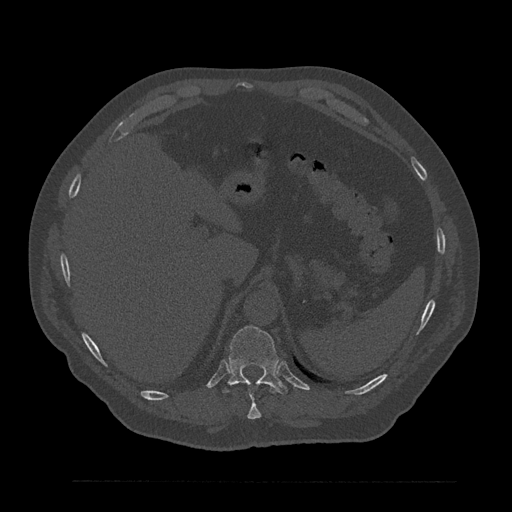
CT including the spine, one axial slice. Position 312 of 797 along the scan axis. 120 kVp. Bone window (W 1800 / L 400 HU). 512 × 512 image matrix, field of view 430 × 430 mm. Patient: male, 61 years. From the clinical record (not read from this slice): primary cancer: prostate.
Outlined on this slice (semi-automatically segmented with operator editing):
- T10 vertebra: box from (x=247, y=392) to (x=262, y=420) px
- T11 vertebra: (x=223, y=326)–(x=288, y=395)